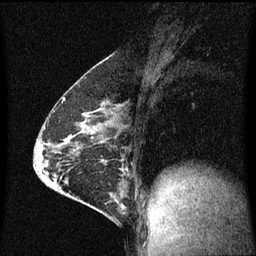
Breast MRI (dynamic contrast-enhanced), one sagittal slice; position 35 of 60 along the scan axis; dynamic contrast-enhanced series, image 2 of 3 at this slice position (ordered by acquisition); 1.5 T; TE 4.2 ms, TR 8 ms; 256 × 256 image matrix. Patient: female, 64 years.
Annotated regions visible in this slice (semi-automatic segmentation, software-assisted and operator-edited):
- analysis volume of interest (the breast-tissue region the enhancement analysis was run in; not a lesion): box from (x=87, y=176) to (x=130, y=217) px
- tumour enhancement mask (voxels above the 70 % enhancement threshold inside the analysis volume of interest): (x=111, y=194)–(x=125, y=209)